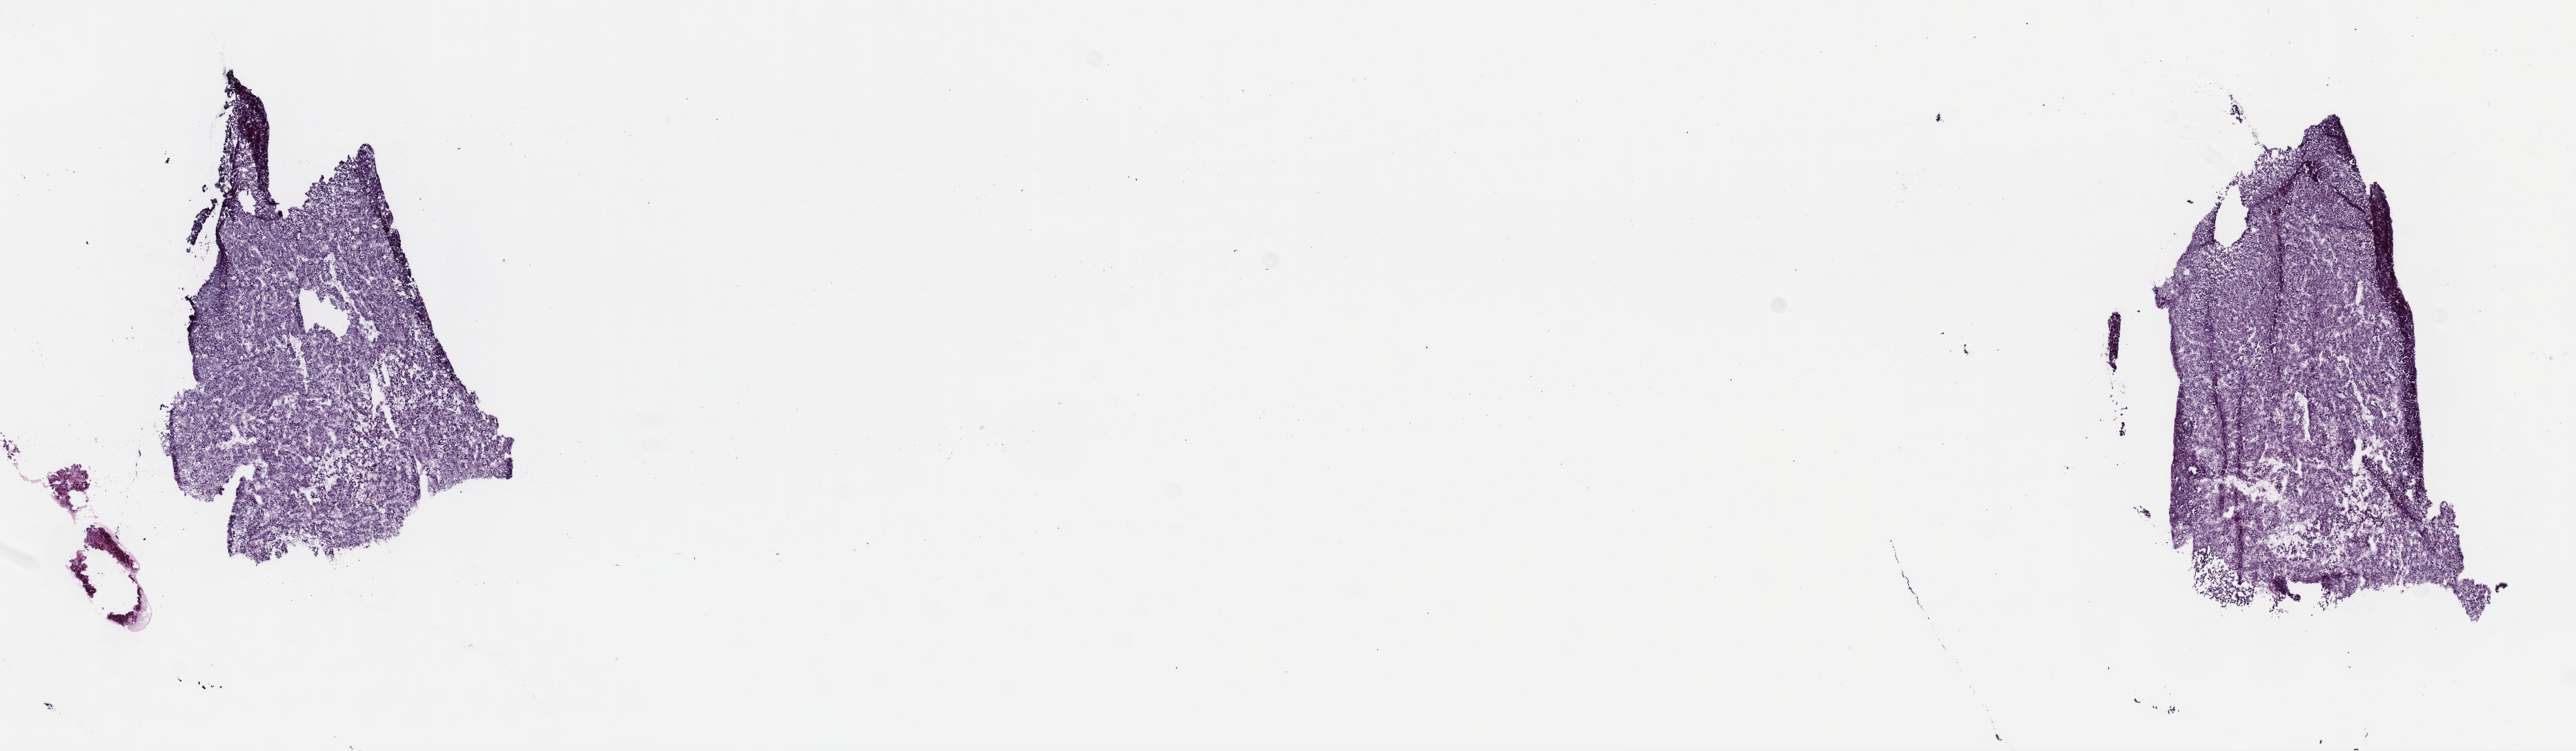
H&E whole-slide image, shown as a low-resolution overview of the whole scanned area (about 15.1 x 4.4 mm); frozen section from the top of the tissue portion; primary tumour sample from the liver. Male, age 56 years at initial diagnosis. Histologic grade: G2 (moderately differentiated). Pathologist review of this section (percent, as recorded): tumour cells 85%, tumour nuclei 85%, normal cells 0%, stromal cells 15%, necrosis 0%. Infiltration values recorded for this section: lymphocyte infiltration 2%, monocyte infiltration 1%, neutrophil infiltration 3%.
Diagnosis: Hepatocellular carcinoma, NOS. AJCC pathologic stage: IIIA (6th edition).